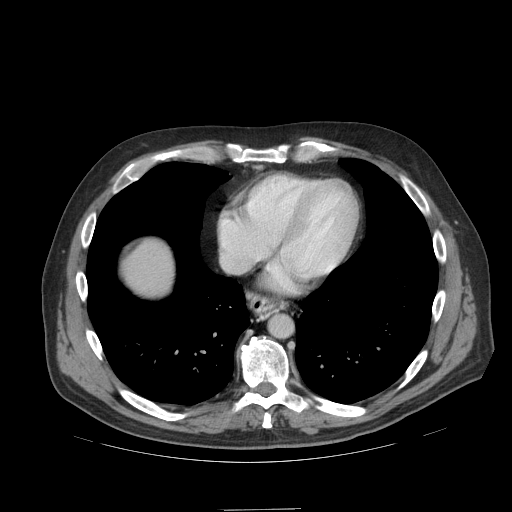
Contrast-enhanced abdominal CT (liver protocol), one axial slice. Position 96 of 99 along the scan axis. 140 kVp. Soft-tissue window (W 400 / L 40 HU). 2.5 mm slice thickness. 512 × 512 image matrix. From the clinical record (not read from this slice): diagnosis: hepatocellular carcinoma (patient treated with transarterial chemoembolisation; whether this scan precedes or follows treatment is not stated here); TNM stage (as recorded): Stage-I; Child-Pugh class: A; tumour differentiation: no biopsy; tumour size: 3.6 cm.
Annotated regions visible in this slice (semi-automatically segmented with operator editing):
- abdominal aorta: box from (x=270, y=315) to (x=292, y=337) px
- liver parenchyma outside the tumour (the mass and vessels are separate outlines, so this box may not span the whole liver): (x=124, y=240)–(x=172, y=294)